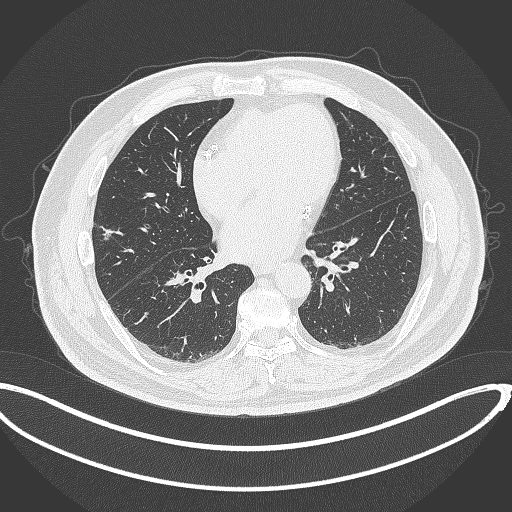
Chest CT, one axial slice. Position 138 of 340 along the scan axis. Reconstruction kernel B70f. 120 kVp. Lung window (W 1500 / L -600 HU). 512 × 512 image matrix, field of view 427 × 427 mm. Male patient, age 68 years. Case-level facts recorded for this patient, not image findings: clinical TNM (as recorded): T1c N0 M0.
Annotated regions visible in this slice (rectangle marked by the reading radiologist):
- lung tumour (recorded histology: adenocarcinoma): box from (x=98, y=223) to (x=117, y=240) px